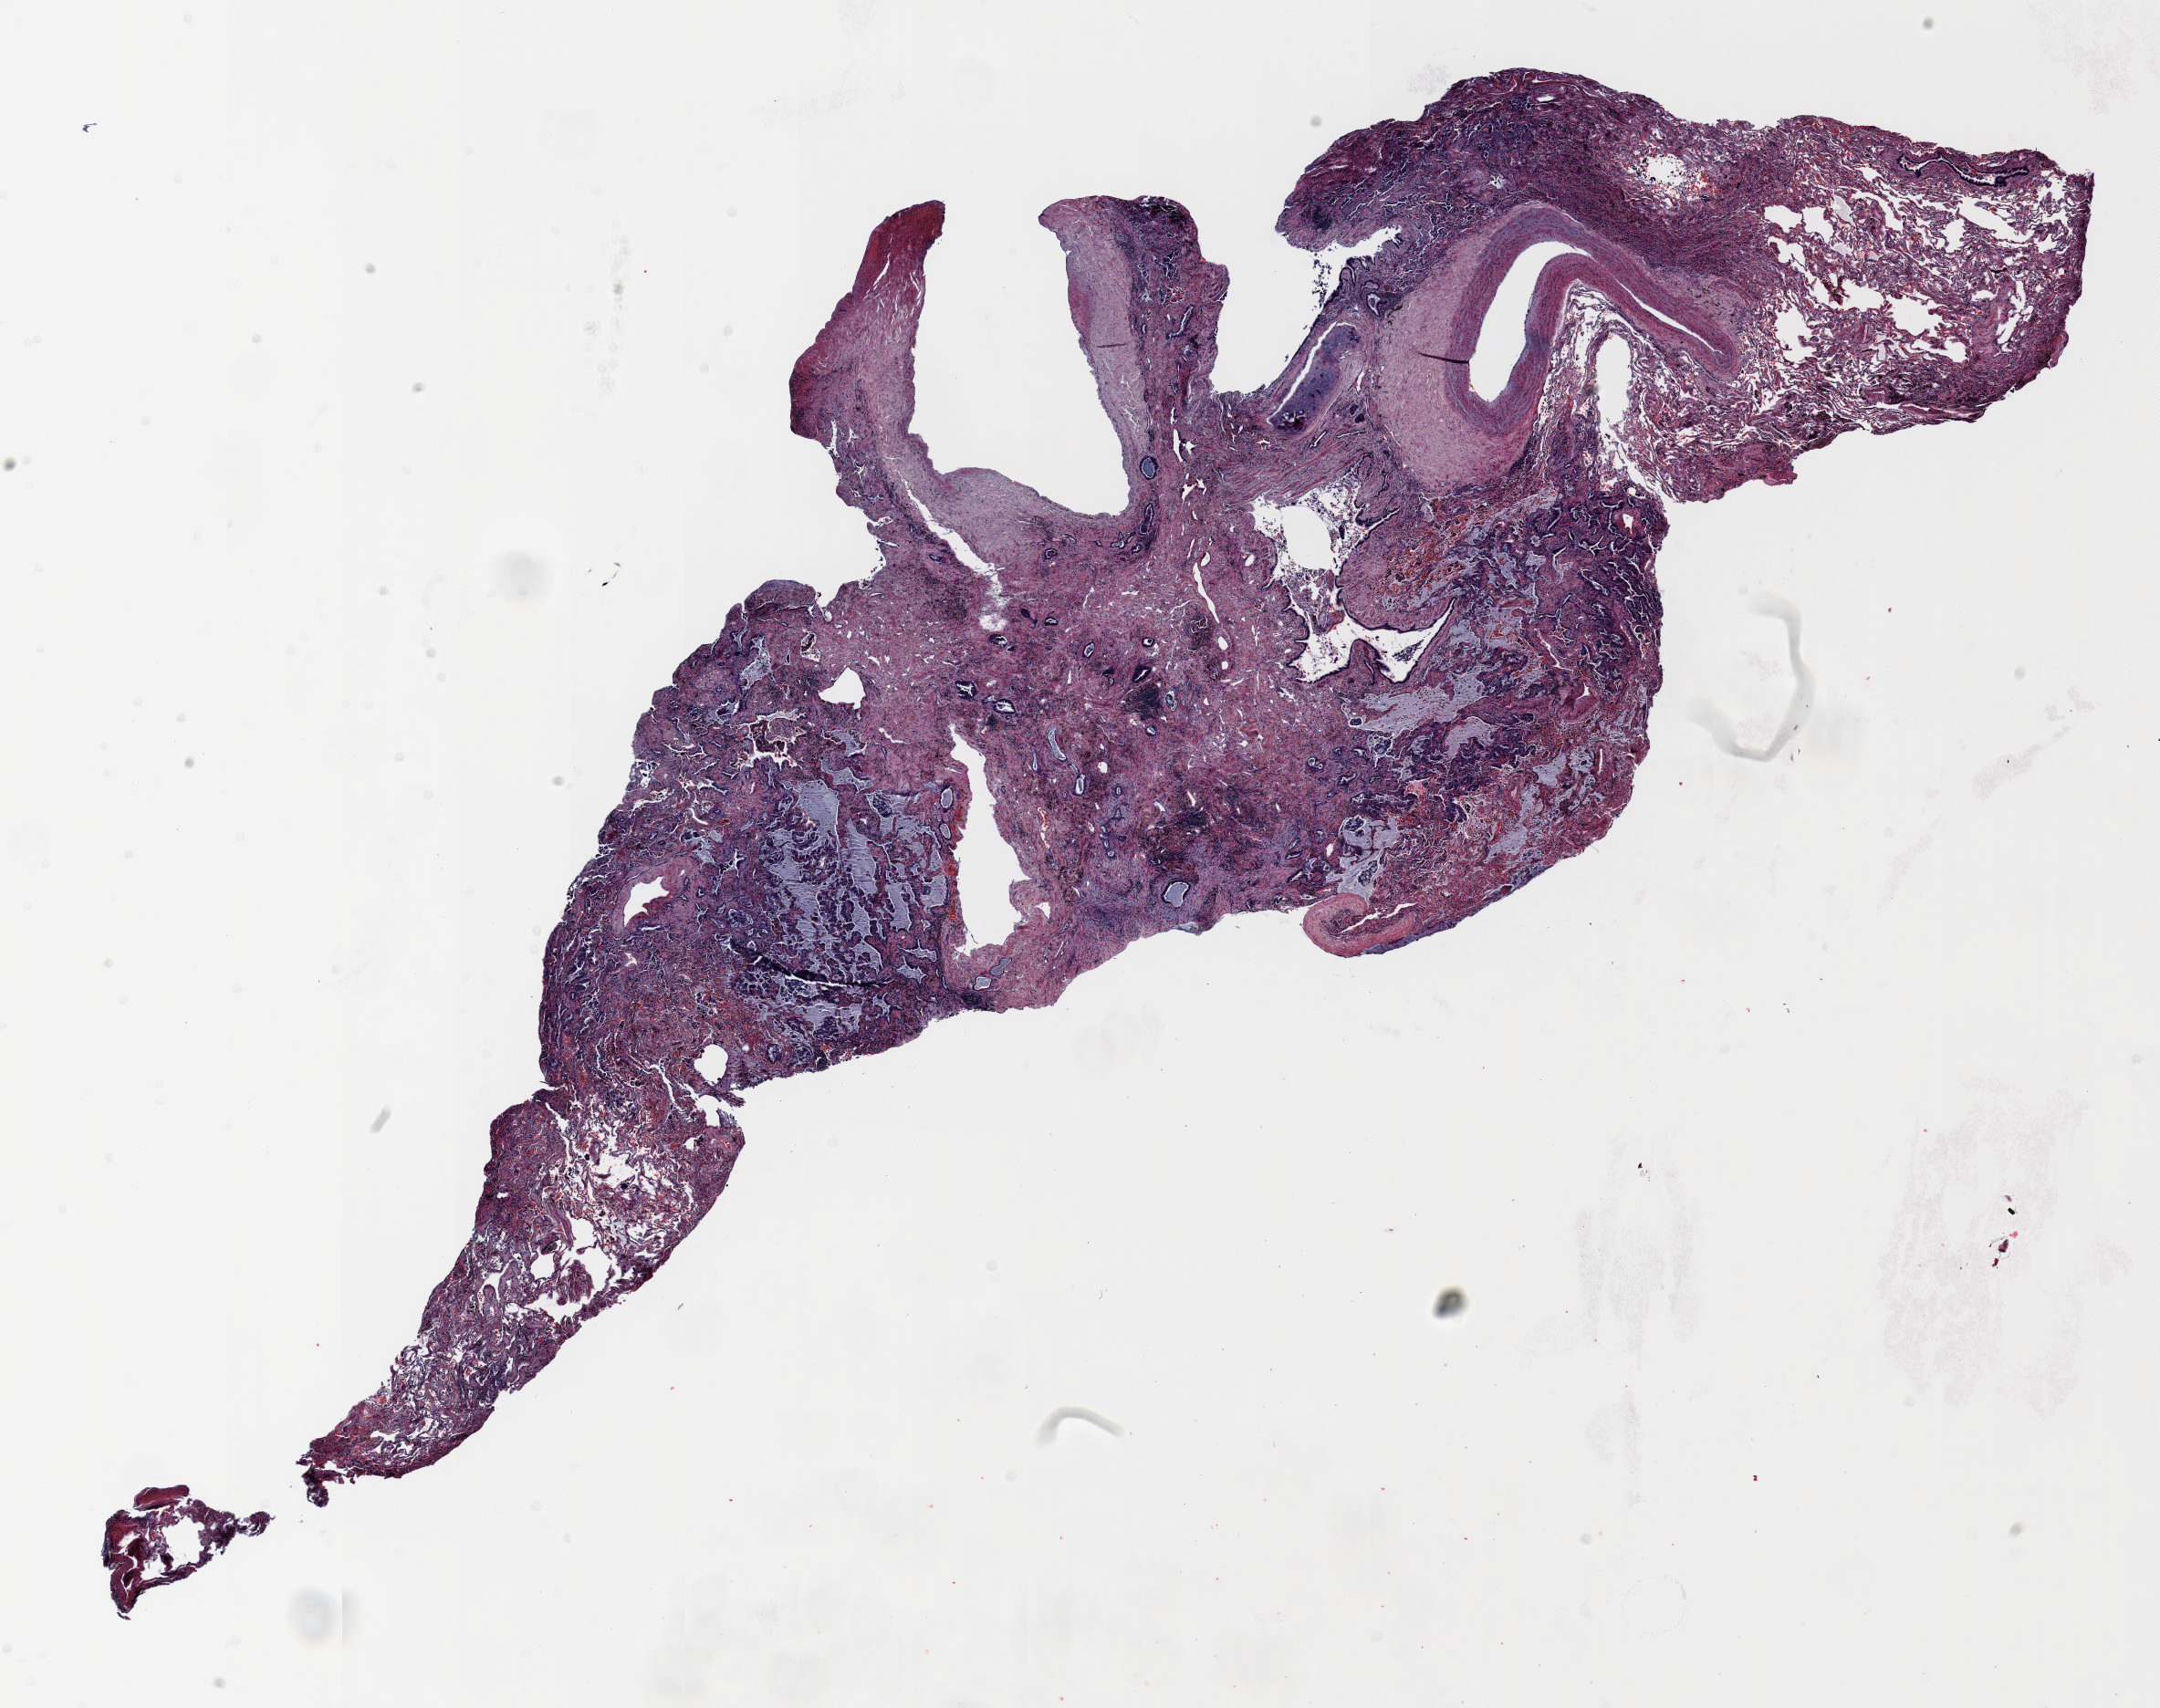
Whole-slide histology image, Hematoxylin and eosin (H&E) stained, low-resolution overview of the scanned area, about 19.0 x 15.0 mm. Formalin-fixed paraffin-embedded (FFPE) section. Lung. Male patient, aged 69 at enrolment. Grade: moderately differentiated (G2).
Primary tumour location (clinical record): right upper lobe. Participant's lung-cancer diagnosis: Mucinous adenocarcinoma (ICD-O-3 8480/3). Tumour size (pathology): 11 mm. Stage (AJCC 6th edition): IA. ICD-O-3 topography: upper lobe of lung (C34.1).